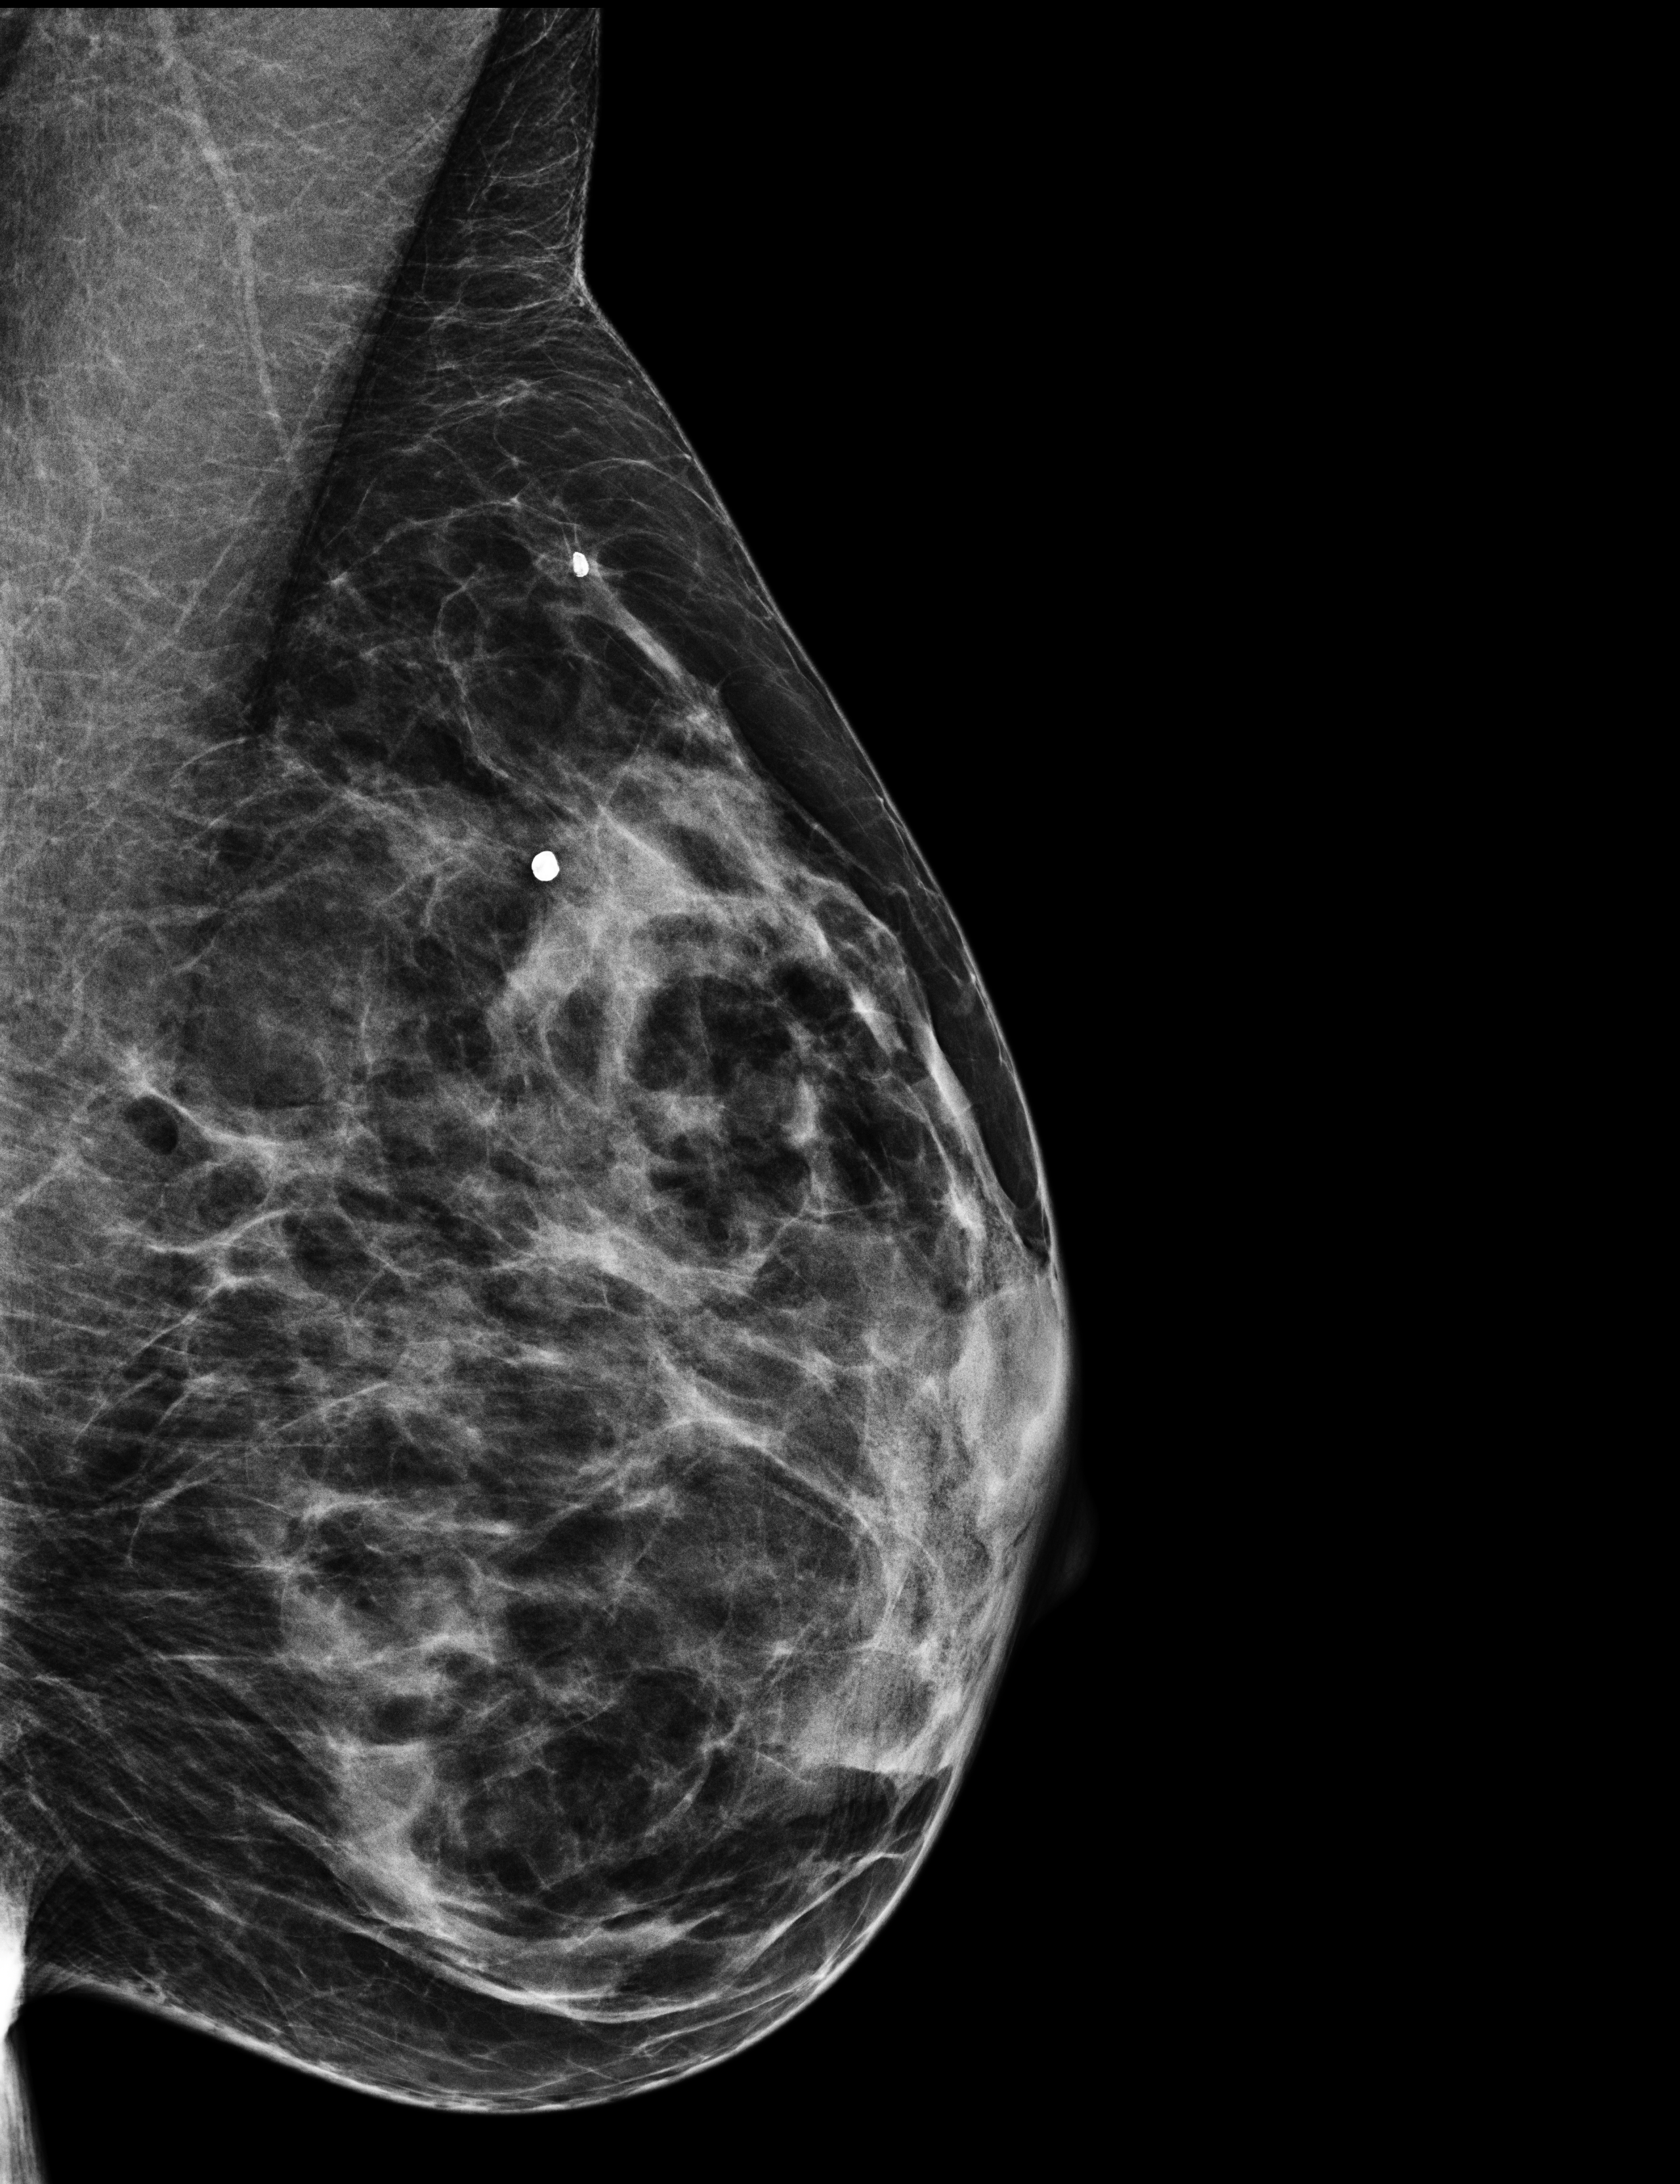
Digital mammogram (FFDM), left breast, MLO view, annual screening mammography examination, compressed breast thickness 36 mm. Patient: female, 54 years.
BI-RADS breast density category at the screening exam (both breasts, scale 1–4): 3. Final BI-RADS category for the screening round (tomosynthesis exam, both breasts): category 1. Recall: no recall after this screen.